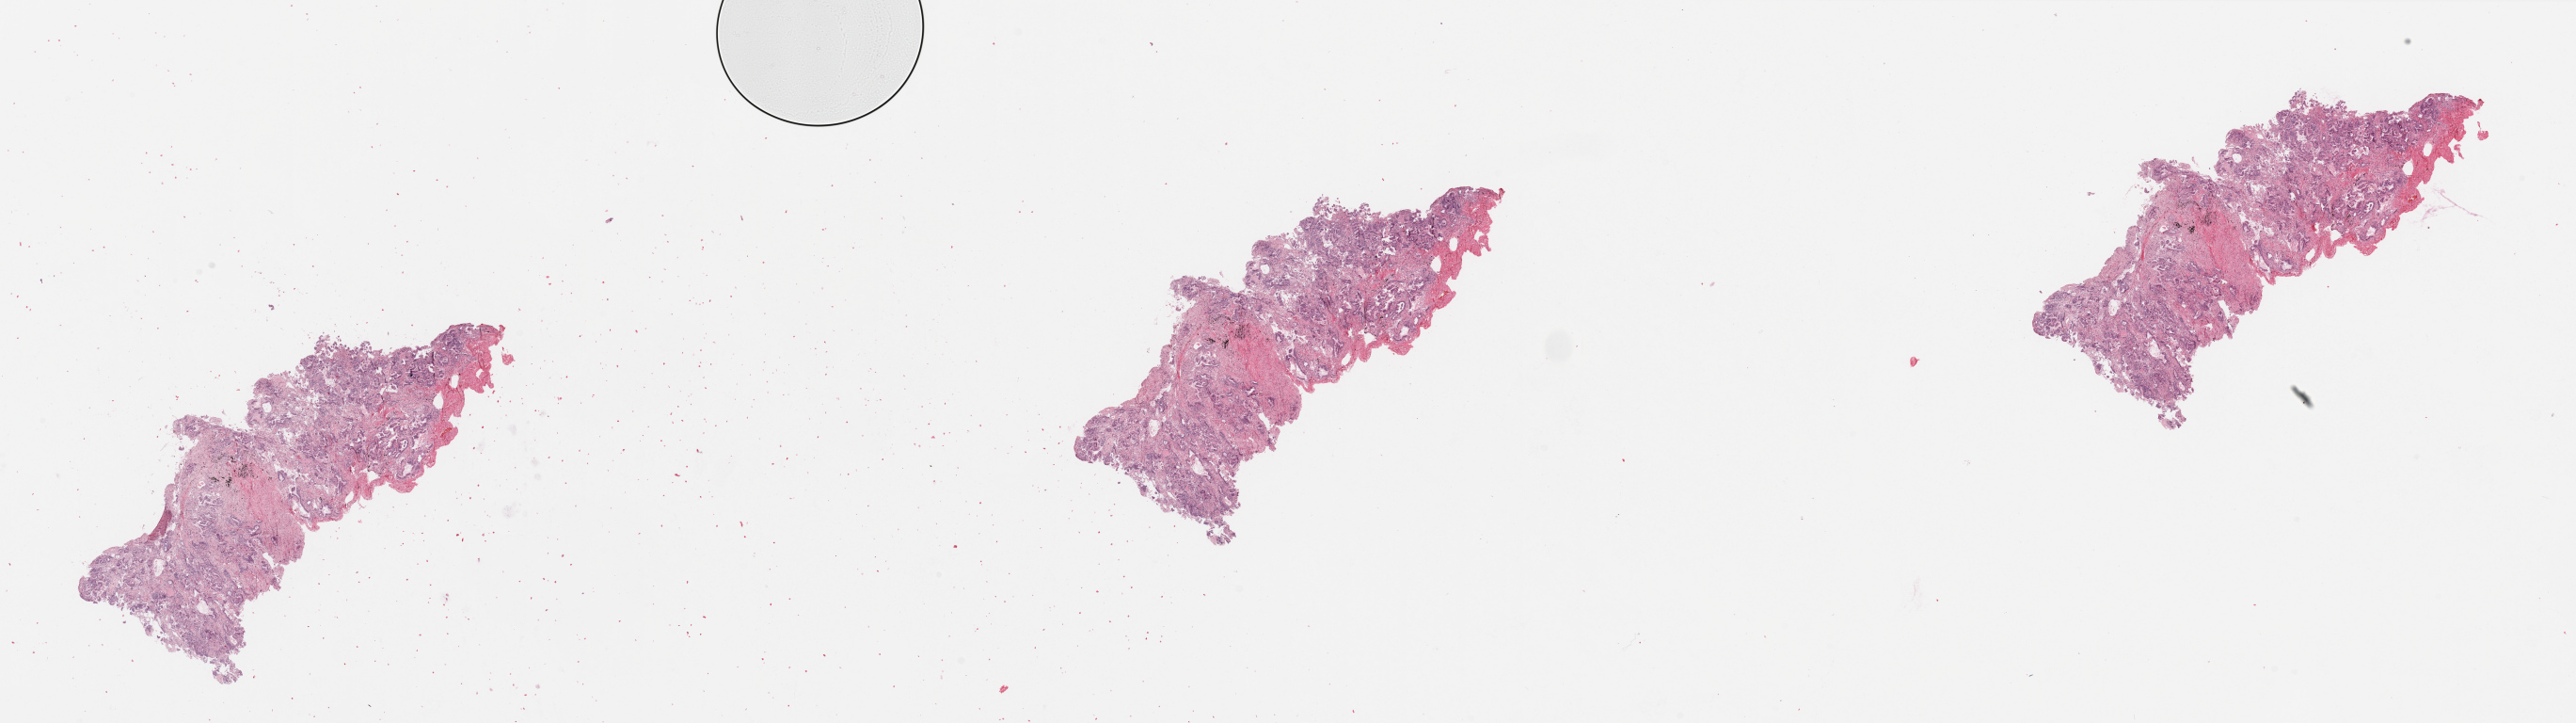
Digitized H&E tissue section (whole slide) — a low-resolution overview of the entire scanned area, about 43.3 x 12.1 mm (slide scanned at 20x). Tumour tissue sample, sampled site: lung. 66-year-old male patient. Histologic grade: G2 (moderately differentiated). Composition of this section per pathologist review: tumour nuclei 70%, necrosis 10%.
Primary tumour site (as recorded): left lower lobe. AJCC pathologic stage: IB. Histologic diagnosis: Adenocarcinoma, NOS.